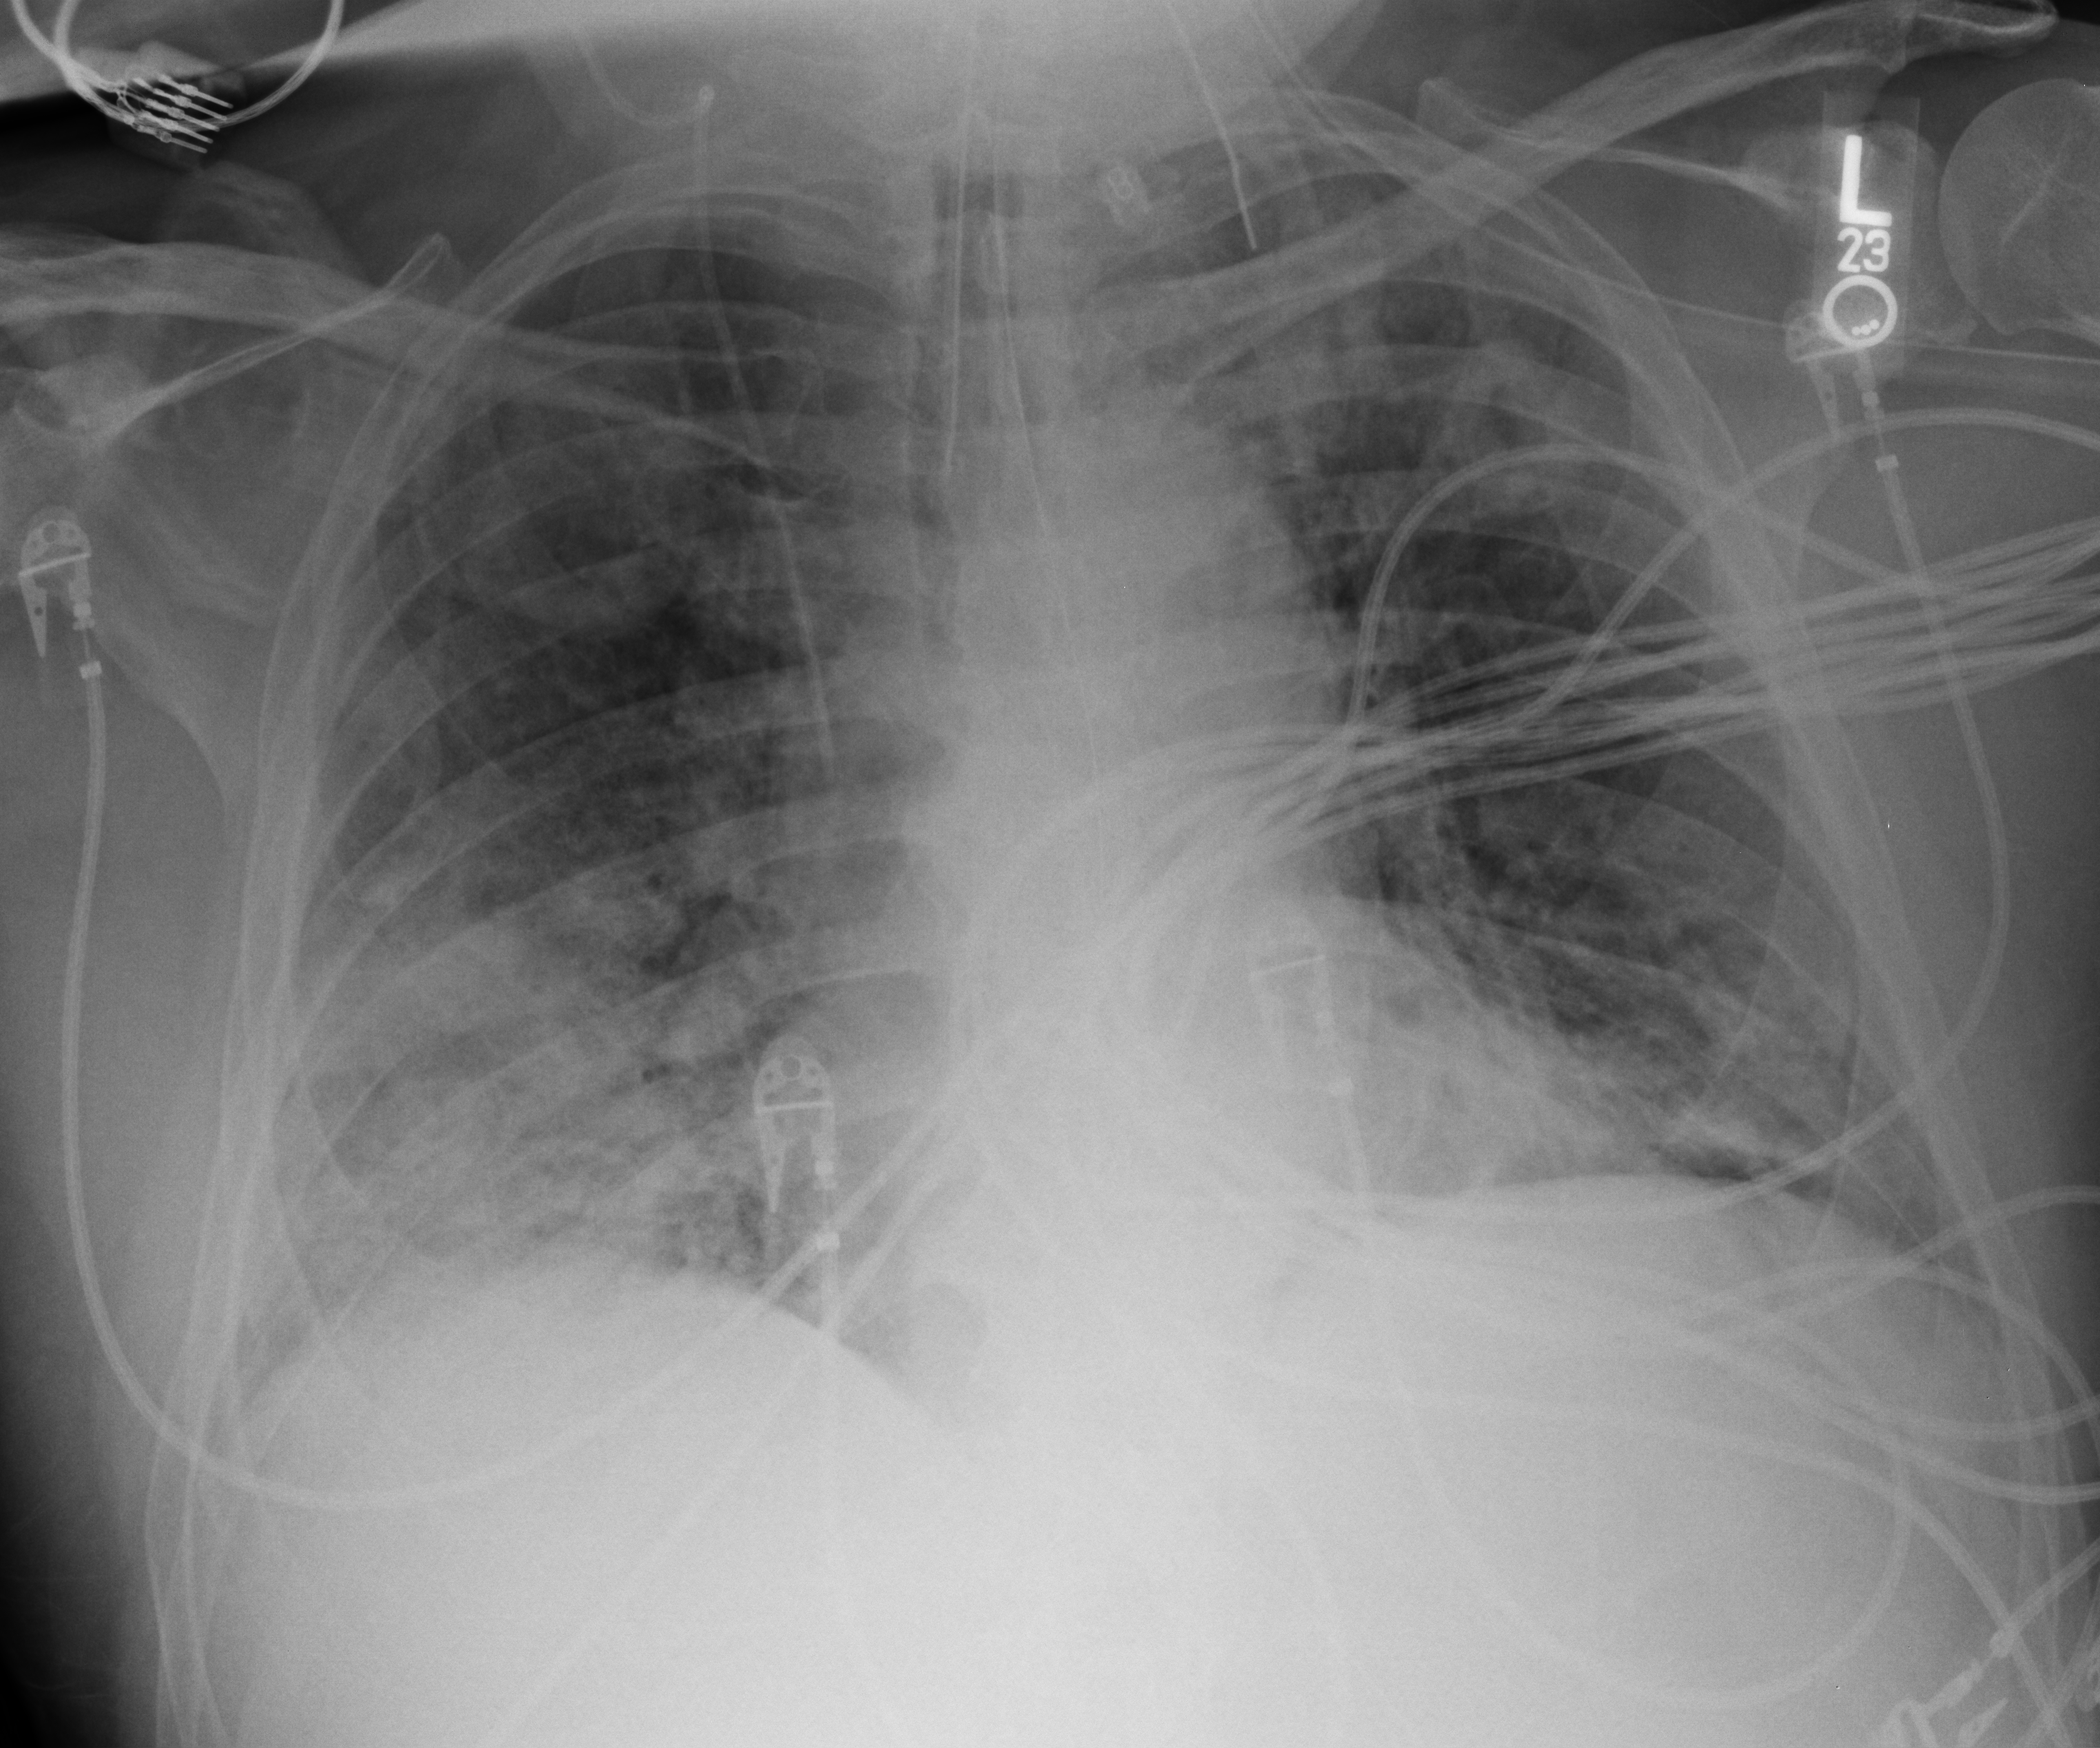
Chest X-ray (portable); anteroposterior (AP) projection. Male patient hospitalised with COVID-19, age 60–74 years.
Hospital-stay facts (about this admission, not read from this image; timing relative to this image not recorded): COPD (admission record): no; chronic kidney disease (admission record): no.